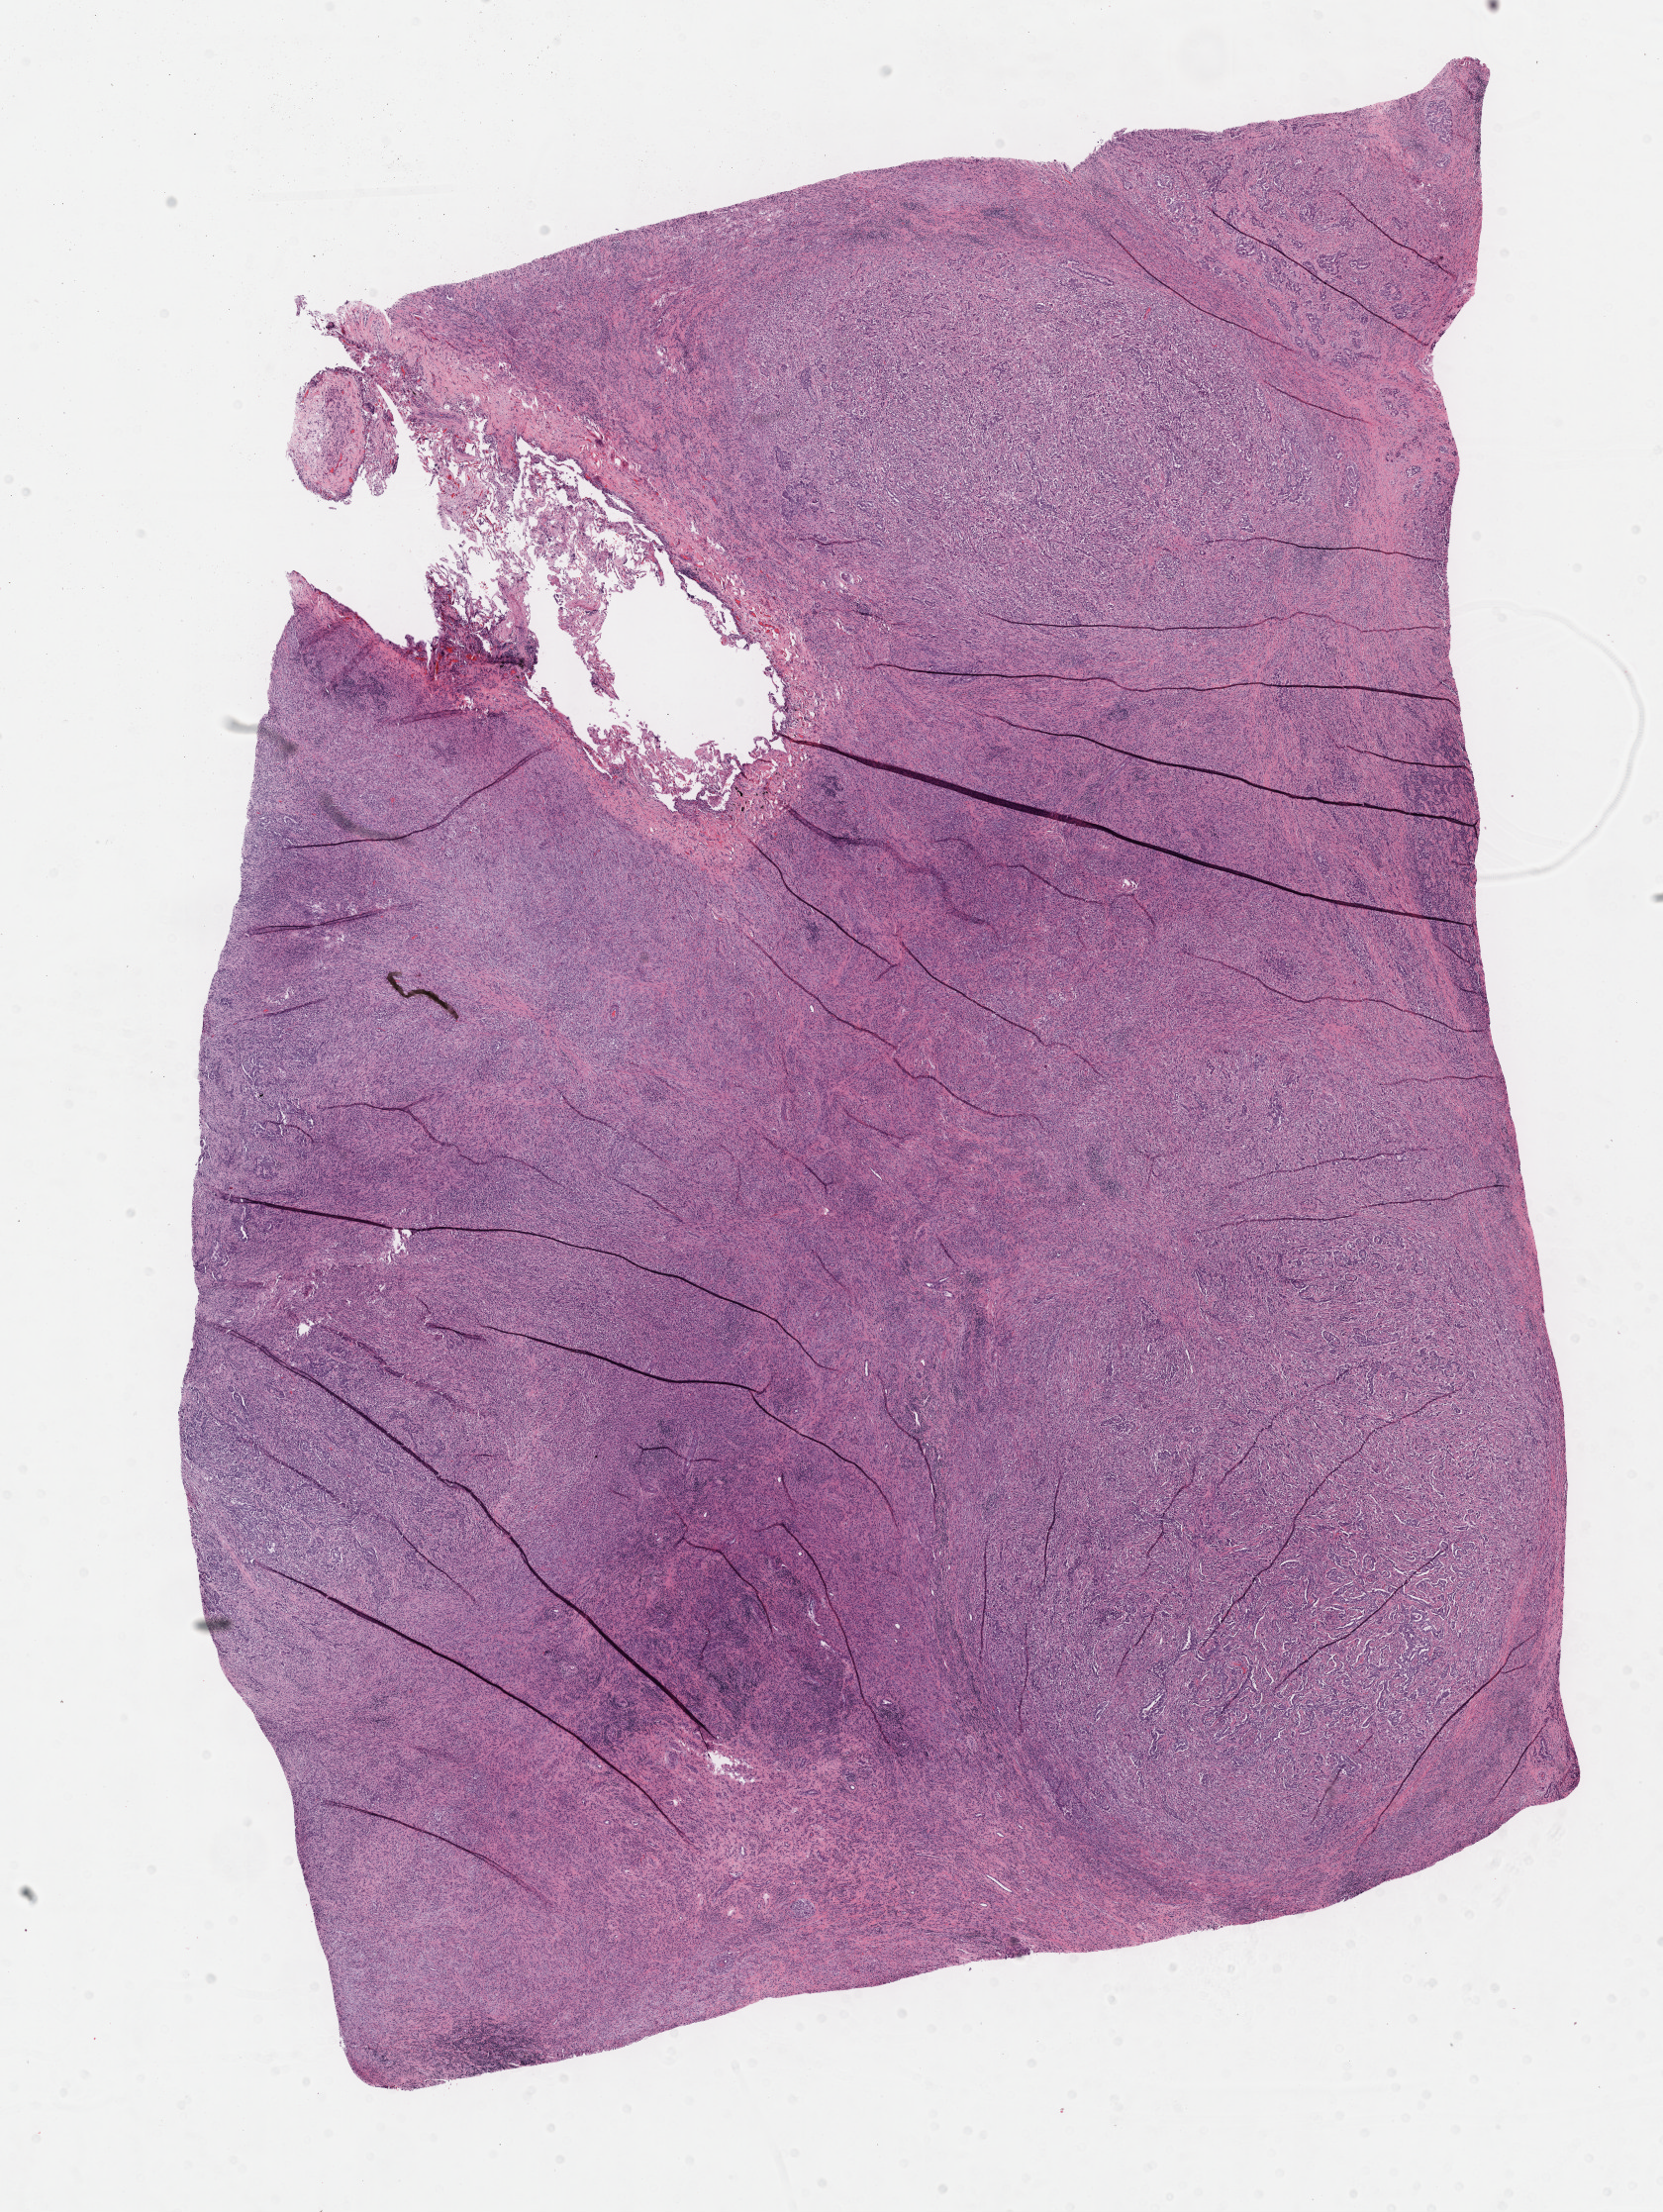
H&E-stained whole-slide image, shown as a low-resolution overview of the whole scanned area (about 13.6 x 18.1 mm, acquisition: 40x scan), FFPE section, mesothelium, primary tumour sample. Patient: male, age at initial diagnosis 80 years.
Pathologic diagnosis: Mesothelioma, biphasic, malignant (pleura, NOS).